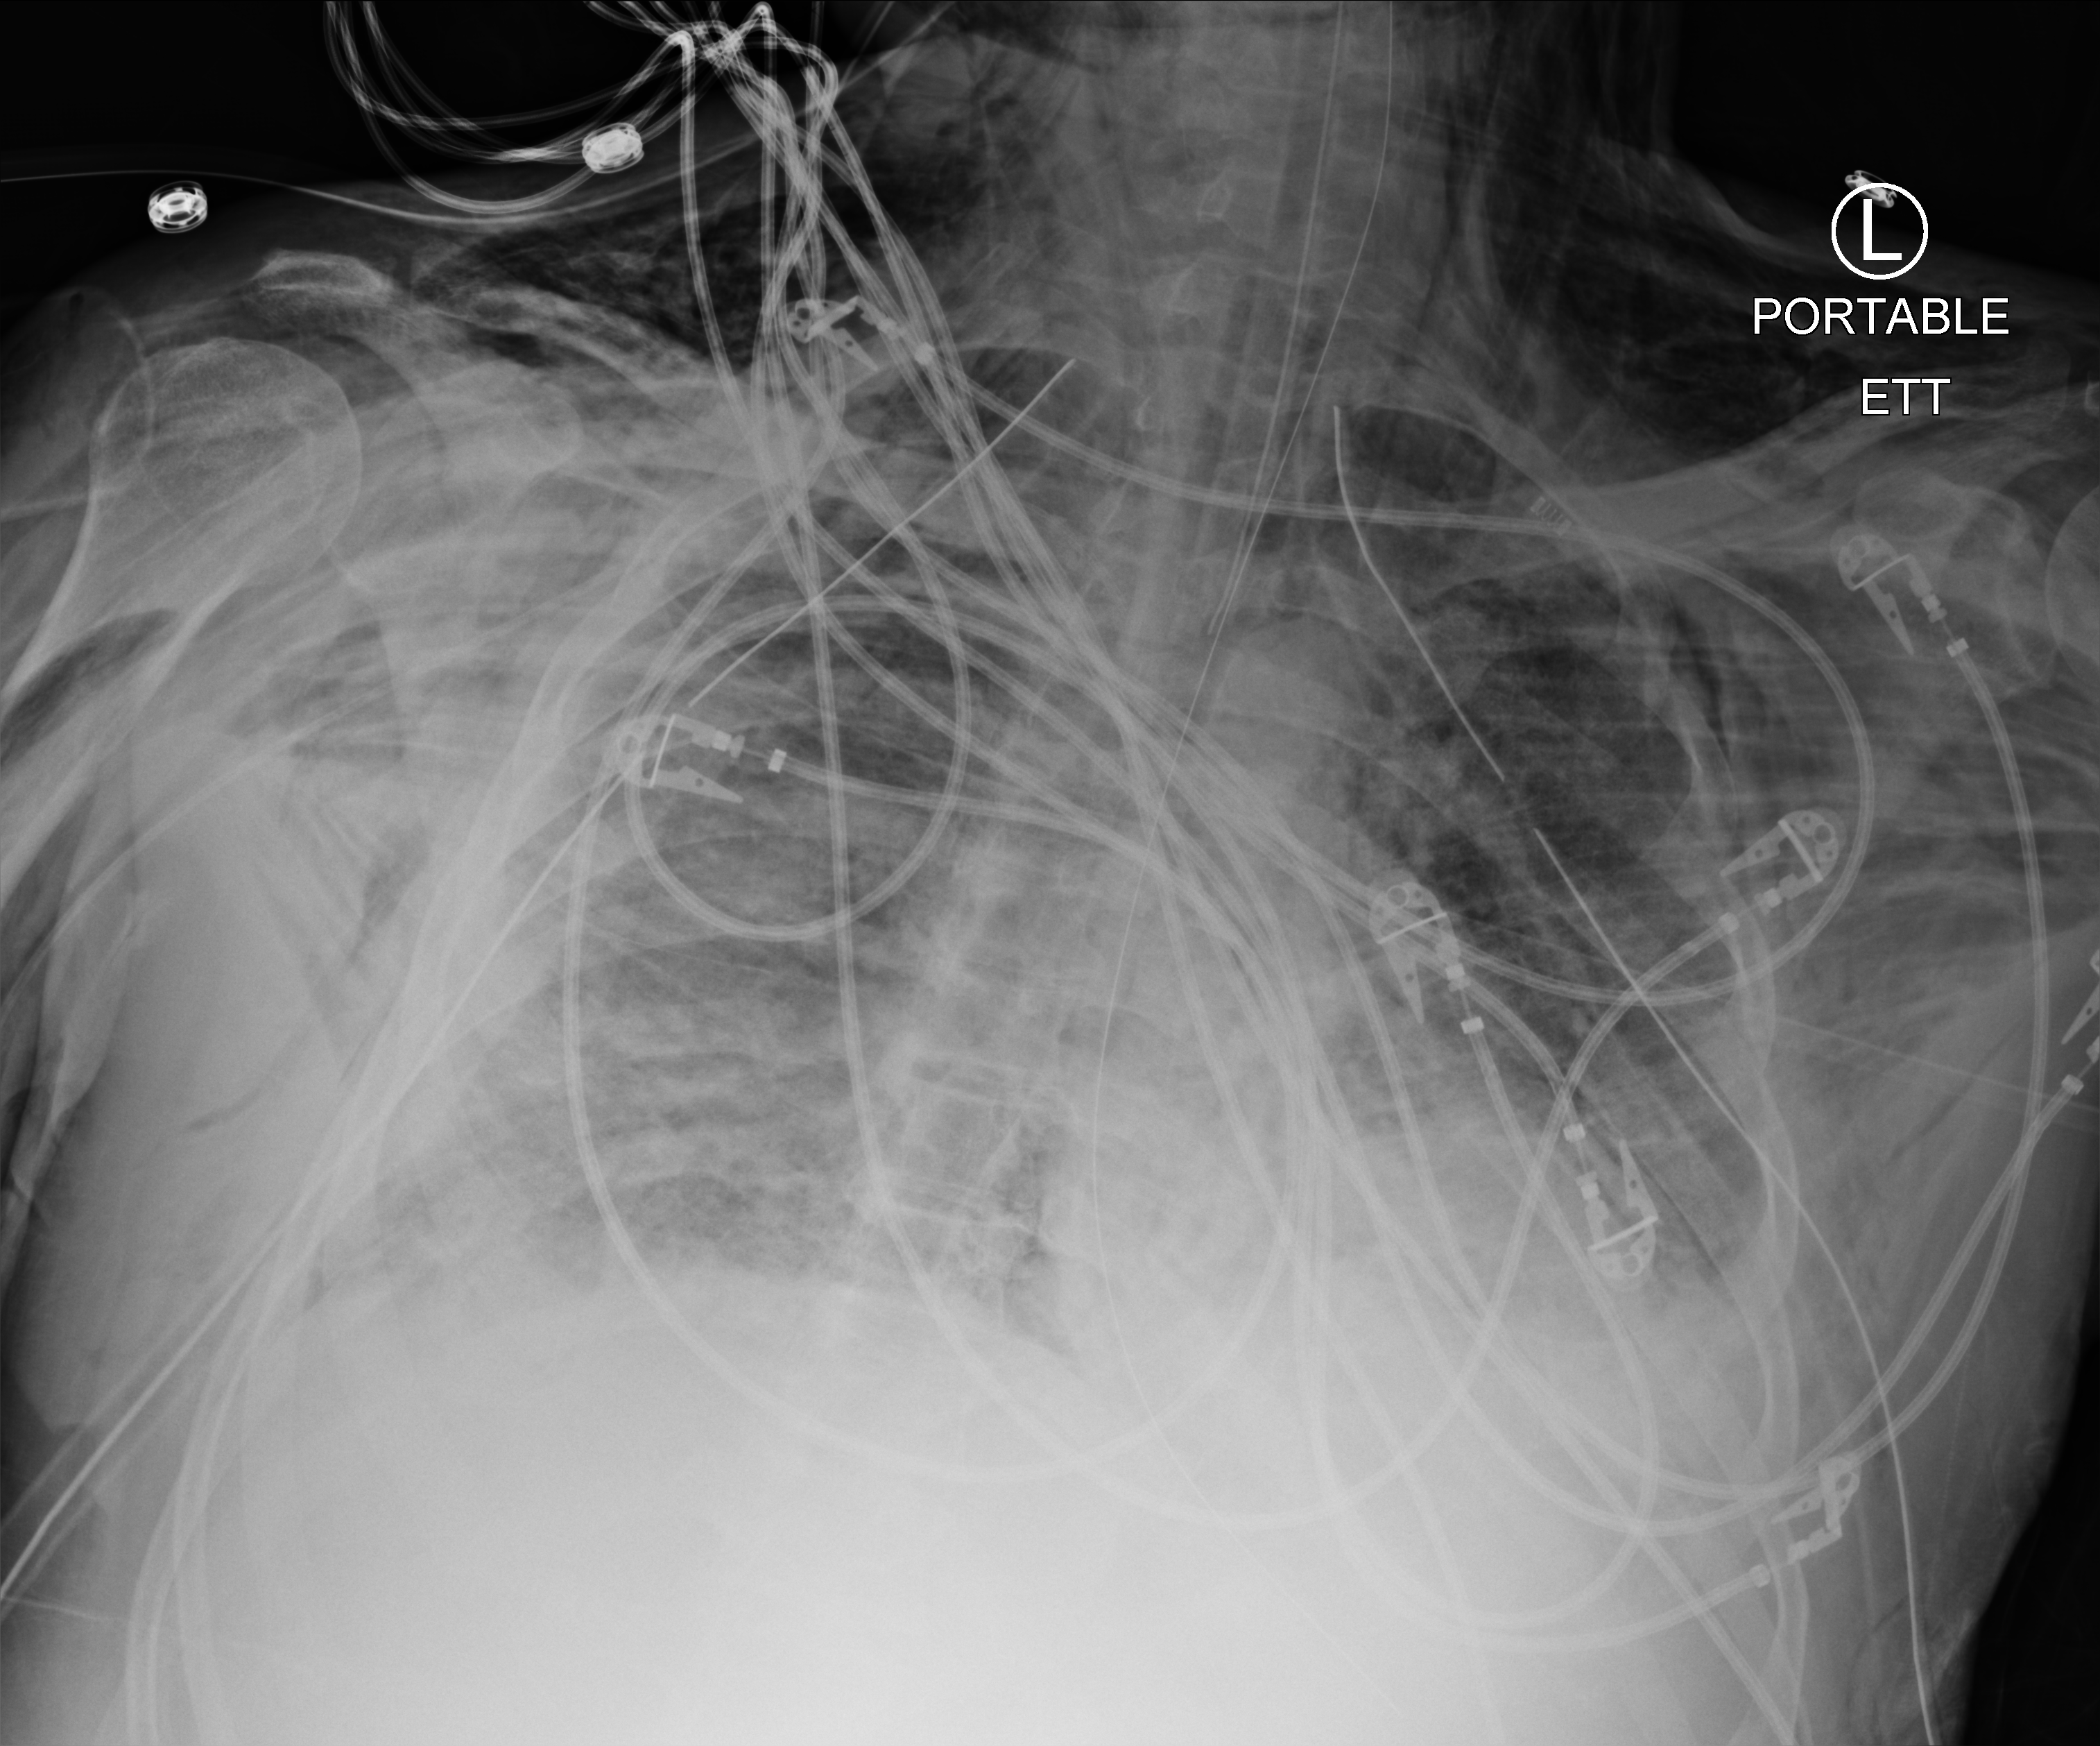
Portable chest radiograph; anteroposterior (AP) projection. Male patient hospitalised with COVID-19, age 18–59 years.
Admission-level facts for this patient (not findings on this image; timing relative to this image not recorded): admitted to intensive care during this hospital stay: yes; COPD (admission record): no.